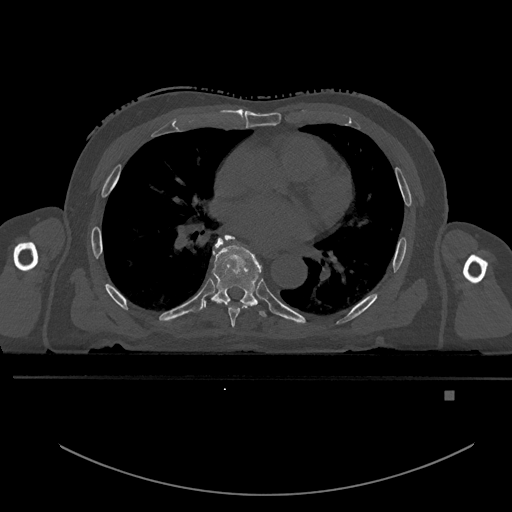
CT including the spine, one axial slice; slice 276 of 969 in the series (ordered by position); bone window (W 1800 / L 400 HU); 0.5 mm slice thickness; 512 × 512 image matrix. Male patient, age 82 years. Case-level facts recorded for this patient, not image findings: primary cancer: prostate; vertebrae with lytic lesions (as recorded): T11, T9, T8, T2.
Structures marked on this image (semi-automatically segmented with operator editing):
- T6 vertebra: bounding box (x1, y1, x2, y2) in pixels: (214, 237, 250, 327)
- T7 vertebra: (203, 235, 266, 317)